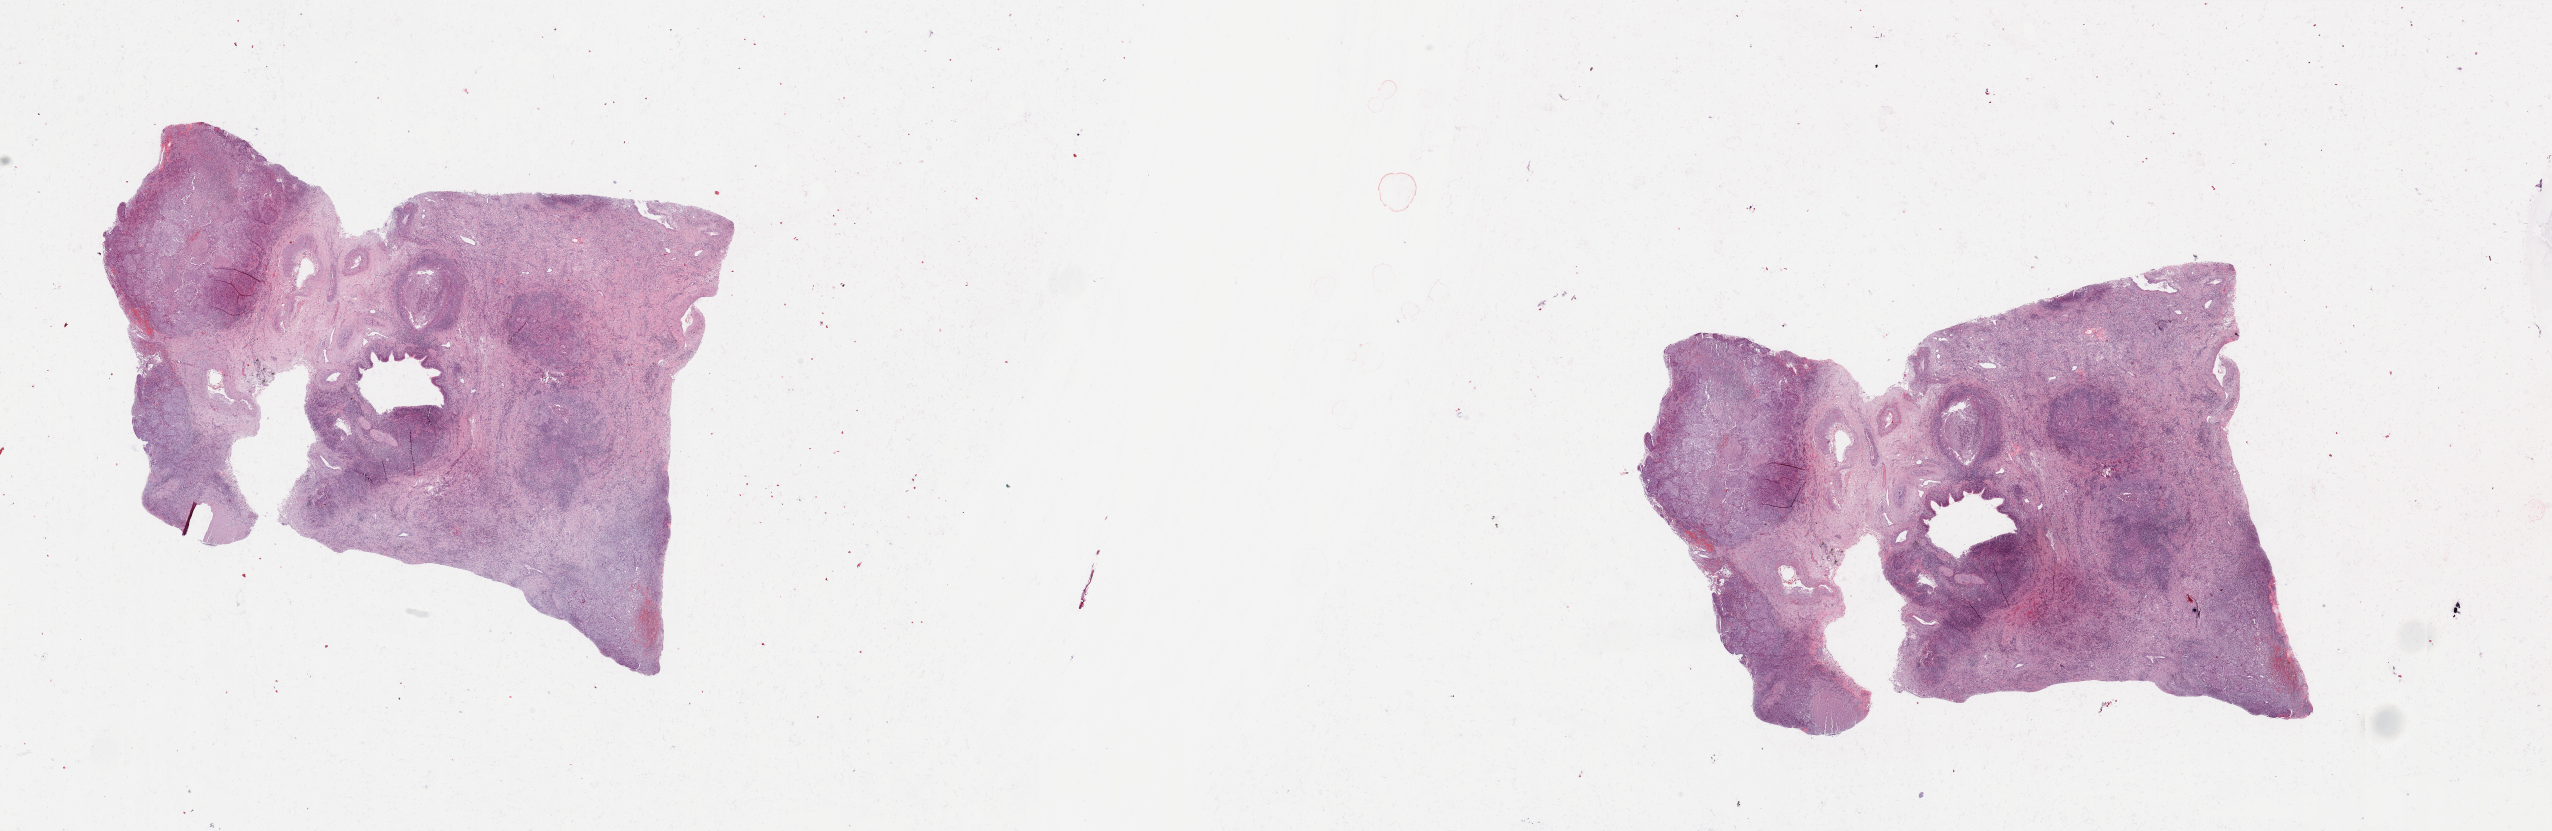
Whole-slide histology image, H&E-stained — whole scanned area (about 40.4 x 13.1 mm) shown as a low-resolution overview, lung, tumour tissue. Male, 57 y/o. Histologic grade: G2 (moderately differentiated).
AJCC pathologic stage: IIB. Diagnosis: Squamous cell carcinoma, NOS. Primary tumour site (as recorded): right lower lobe.